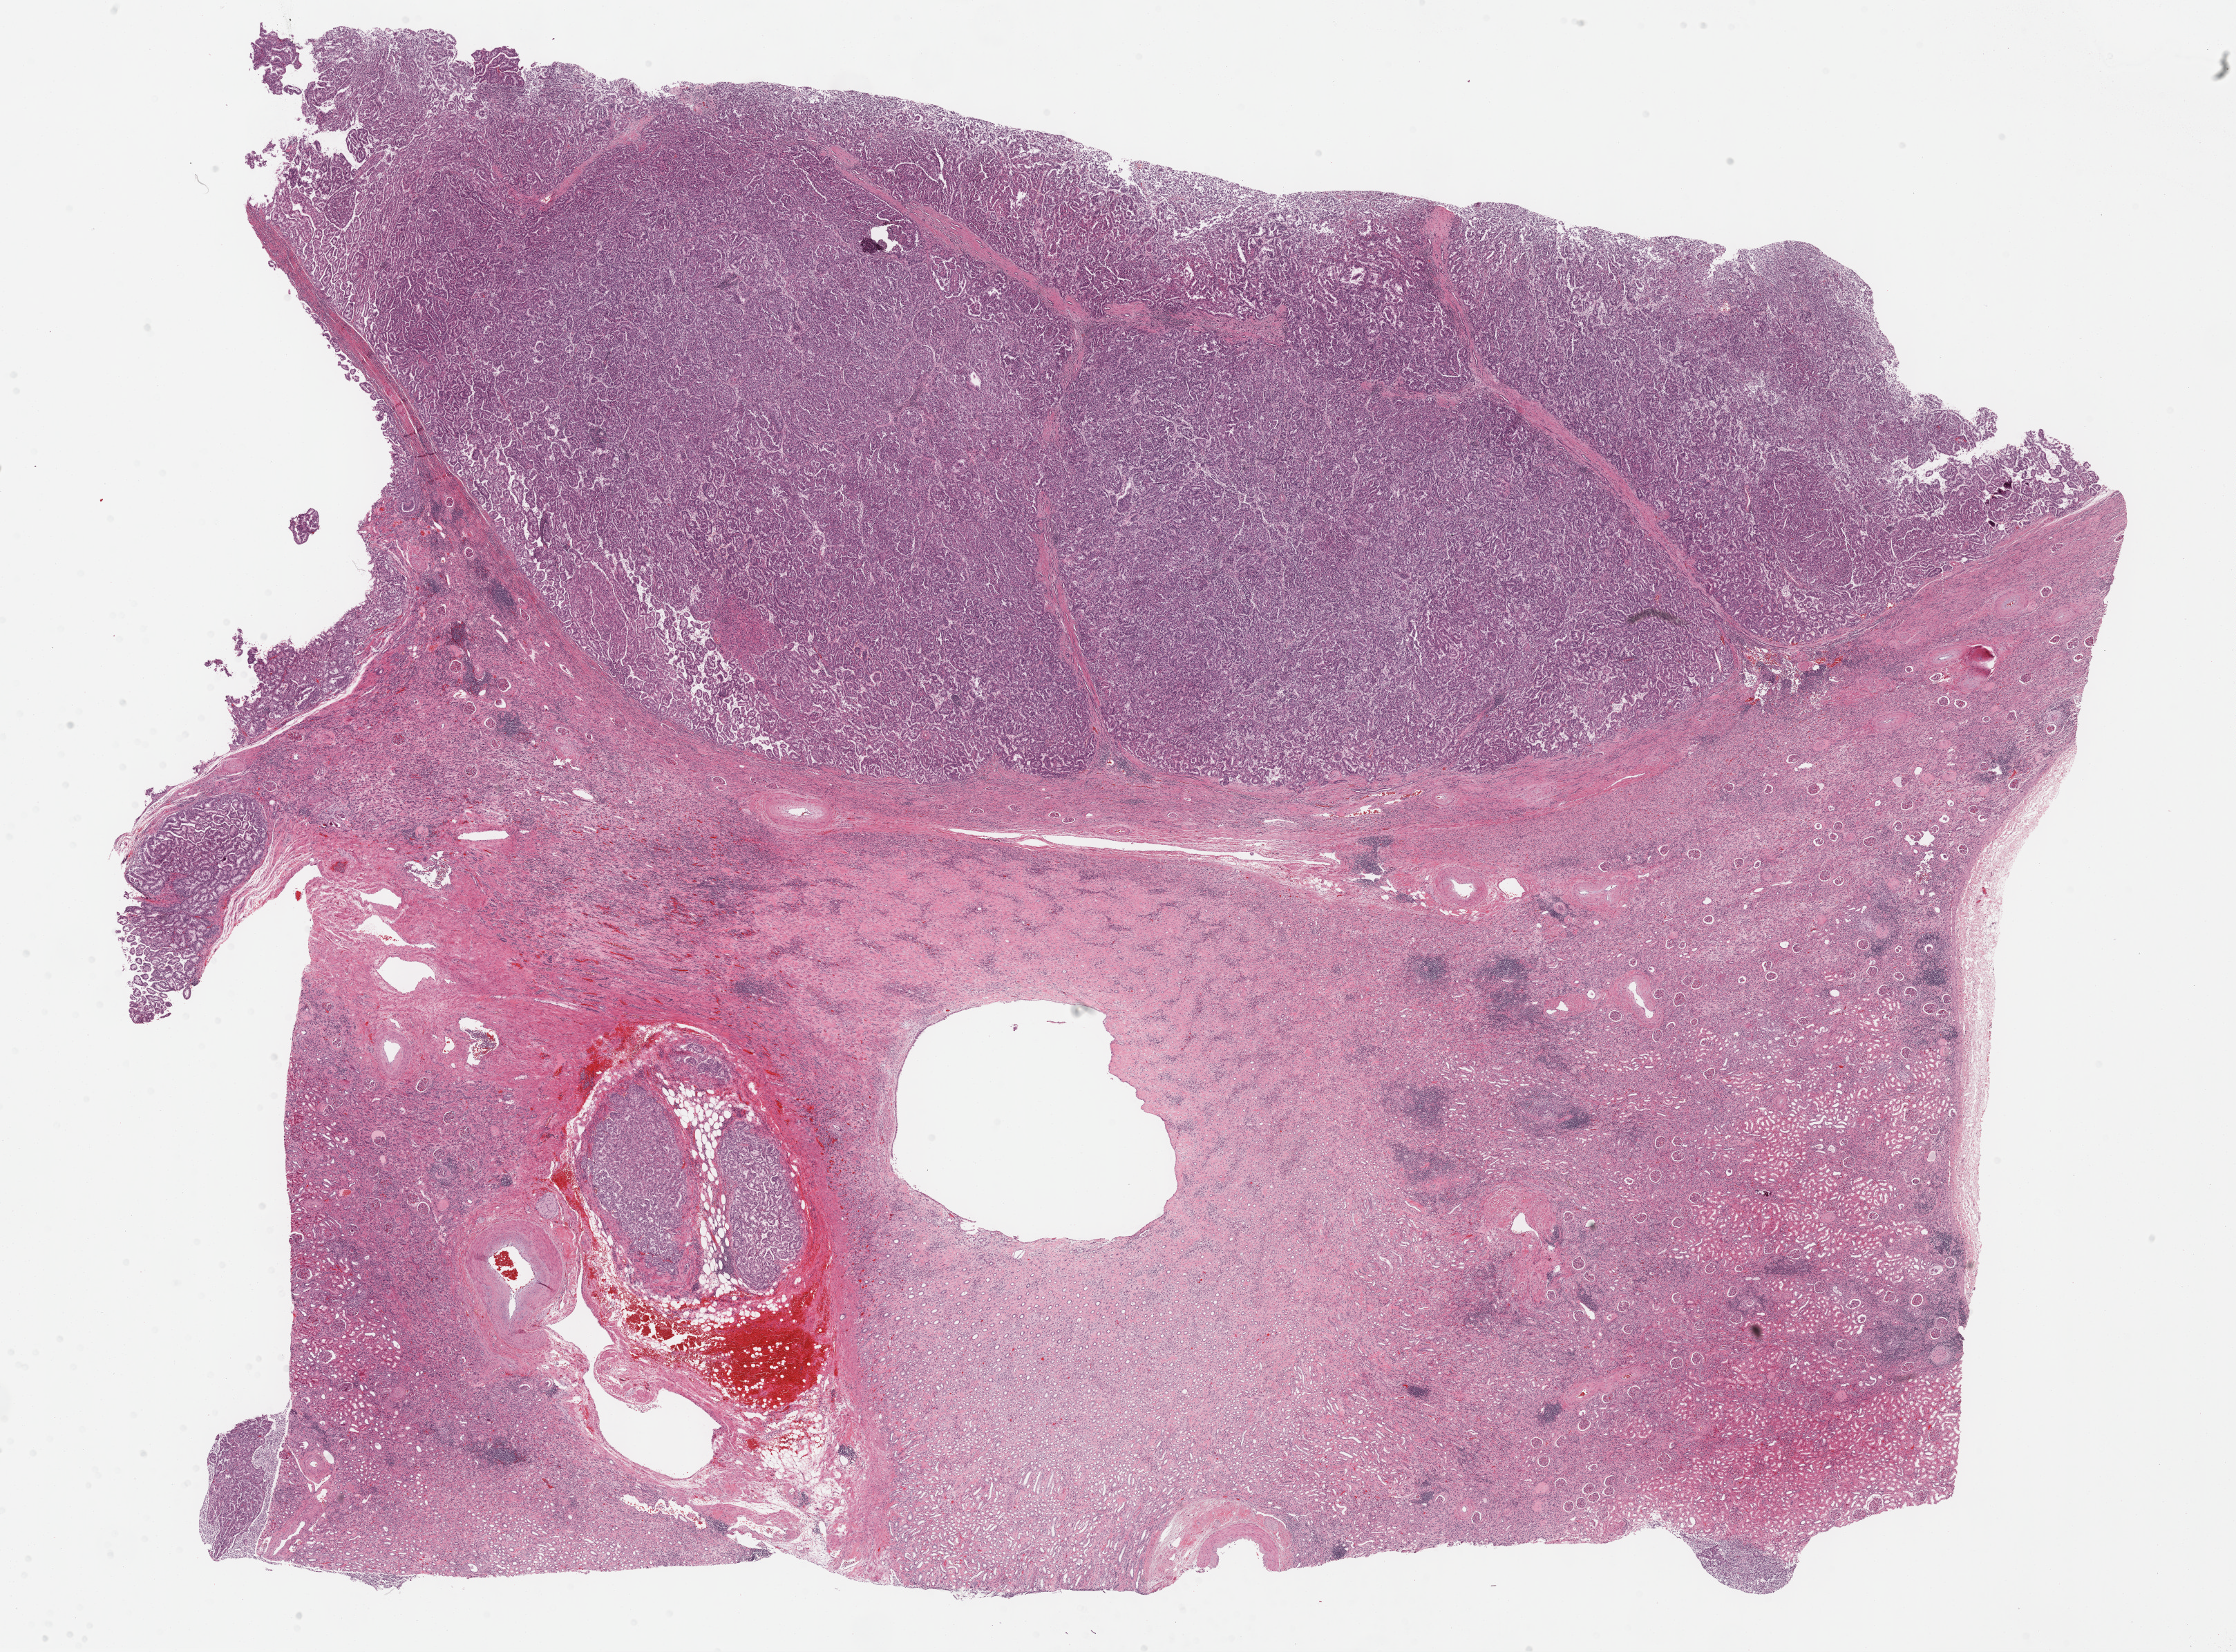
Whole-slide histology image, H&E-stained, low-resolution overview of the scanned area, about 26.2 x 19.3 mm (slide scanned at 40x). Formalin-fixed paraffin-embedded (FFPE) diagnostic section. Sample: primary tumour, kidney. Male patient; age at initial diagnosis 62 years.
• AJCC pathologic stage: III (7th edition)
• diagnosis: Papillary adenocarcinoma, NOS